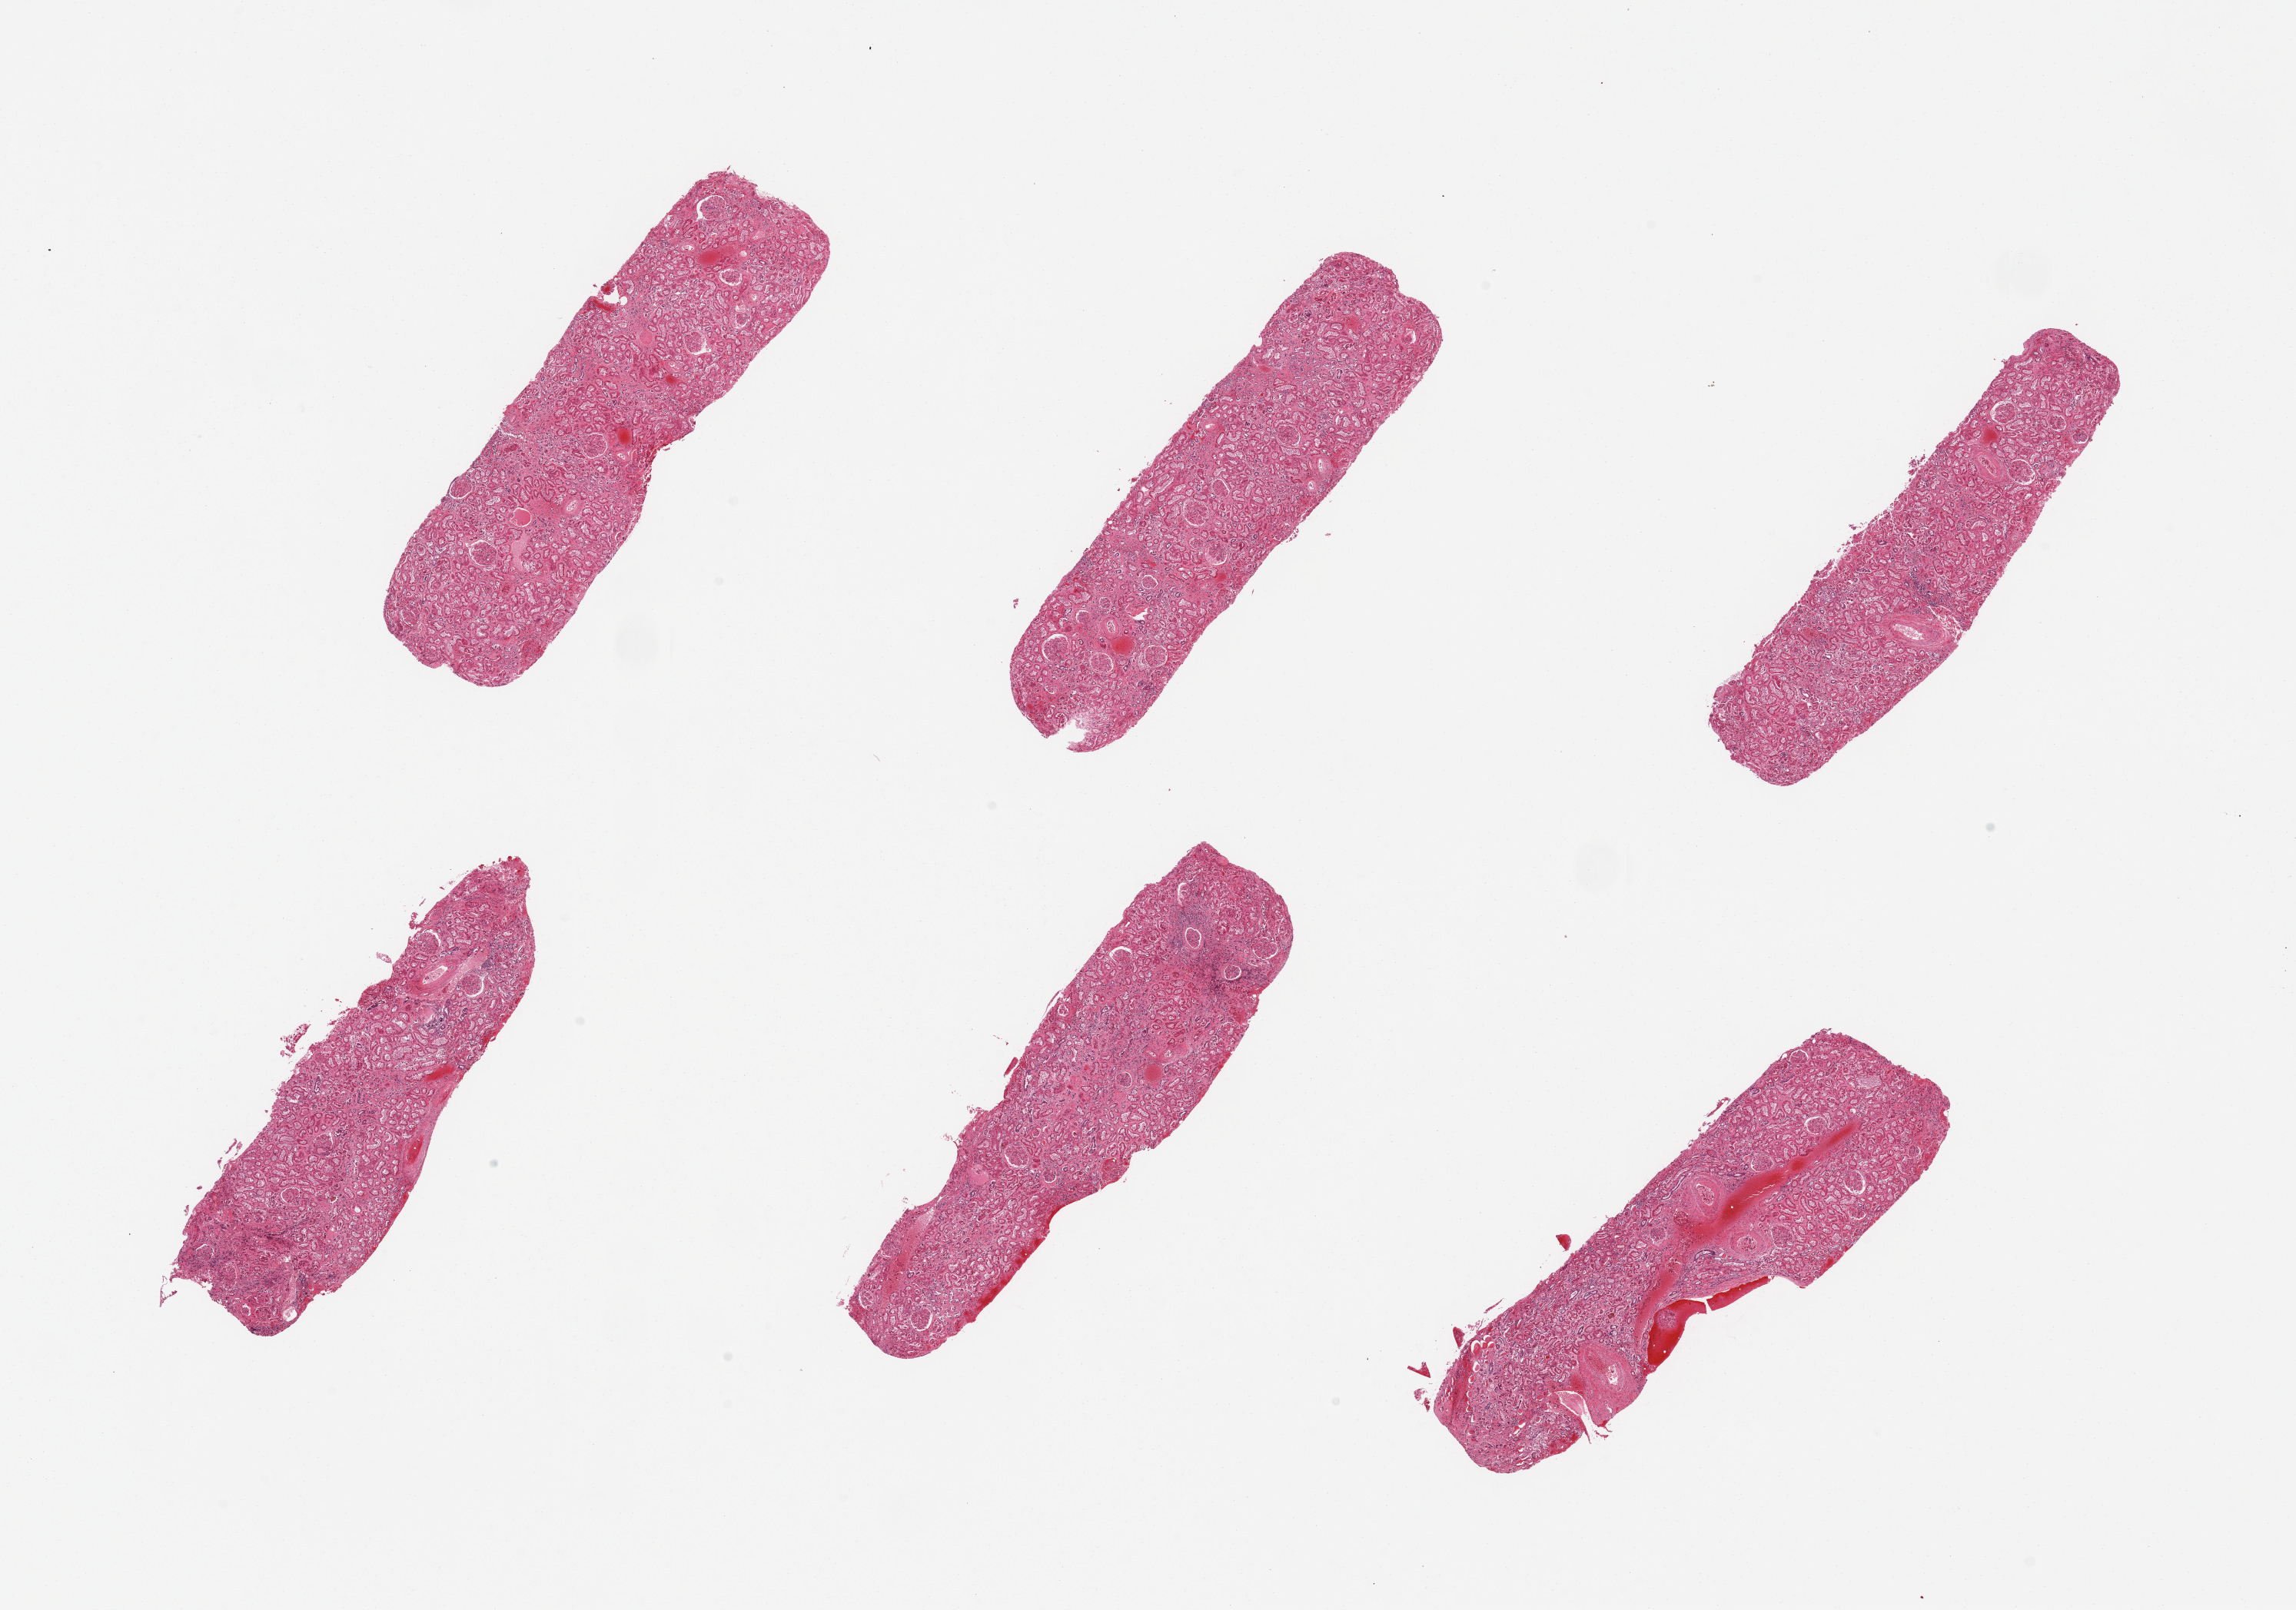
Whole-slide image, haematoxylin and eosin stain — low-resolution overview of the scanned area, about 23.6 x 16.6 mm, PAXgene-fixed, paraffin-embedded tissue, sampled site (target tissue): renal cortex, donor tissue sample.
• pathologist's review note for this sample: 6 pieces; glomeruli present, tubules with moderate - advanced autolysis